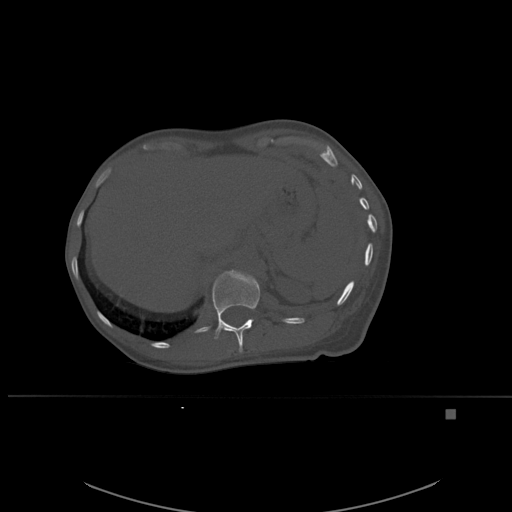
CT including the spine, one axial slice; slice 278 of 537 in the series (ordered by position); bone window (W 1800 / L 400 HU); 1.5 mm slice thickness; 512 × 512 image matrix. Female patient, age 45 years. From the clinical record (not read from this slice): primary cancer: lung.
Annotated regions visible in this slice (semi-automatic segmentation, software-assisted and operator-edited):
- T12 vertebra: bounding box [x1, y1, x2, y2] px = [212, 269, 260, 353]